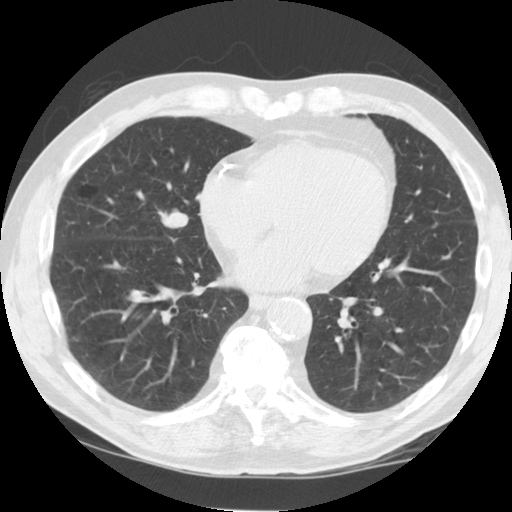
Low-dose screening chest CT, one axial slice; slice 44 of 125 in the series (ordered by position); reconstruction kernel STANDARD; 120 kVp; lung window (W 1500 / L -600 HU); 2.5 mm slice thickness; 512 × 512 image matrix, field of view 350 × 350 mm.
Annotated regions visible in this slice (manually delineated by an expert):
- lesion 1 (tumor, middle lobe of right lung): bounding box <159,212,188,228> (left, top, right, bottom; pixels)